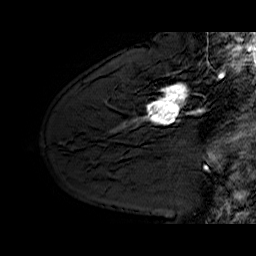
Breast MRI (dynamic contrast-enhanced), one sagittal slice; slice 44 of 60 in the series (ordered by position); dynamic contrast-enhanced series, time point 2 of 6 at this slice position (early post-contrast); 1.5 T; TE 6.4 ms, TR 32.9 ms; 4 mm slice thickness; 256 × 256 image matrix, field of view 200 × 200 mm. Female patient. From the clinical record (not read from this slice): setting: breast cancer imaged before/during neoadjuvant chemotherapy; receptor status: HER2-positive.
Outlined on this slice (semi-automatic segmentation, software-assisted and operator-edited):
- analysis volume of interest (the breast-tissue region the enhancement analysis was run in; not a lesion): bounding box <130,62,210,127> (left, top, right, bottom; pixels)
- tumour enhancement mask (voxels above the 100 % enhancement threshold inside the analysis volume of interest): <142,84,200,124>